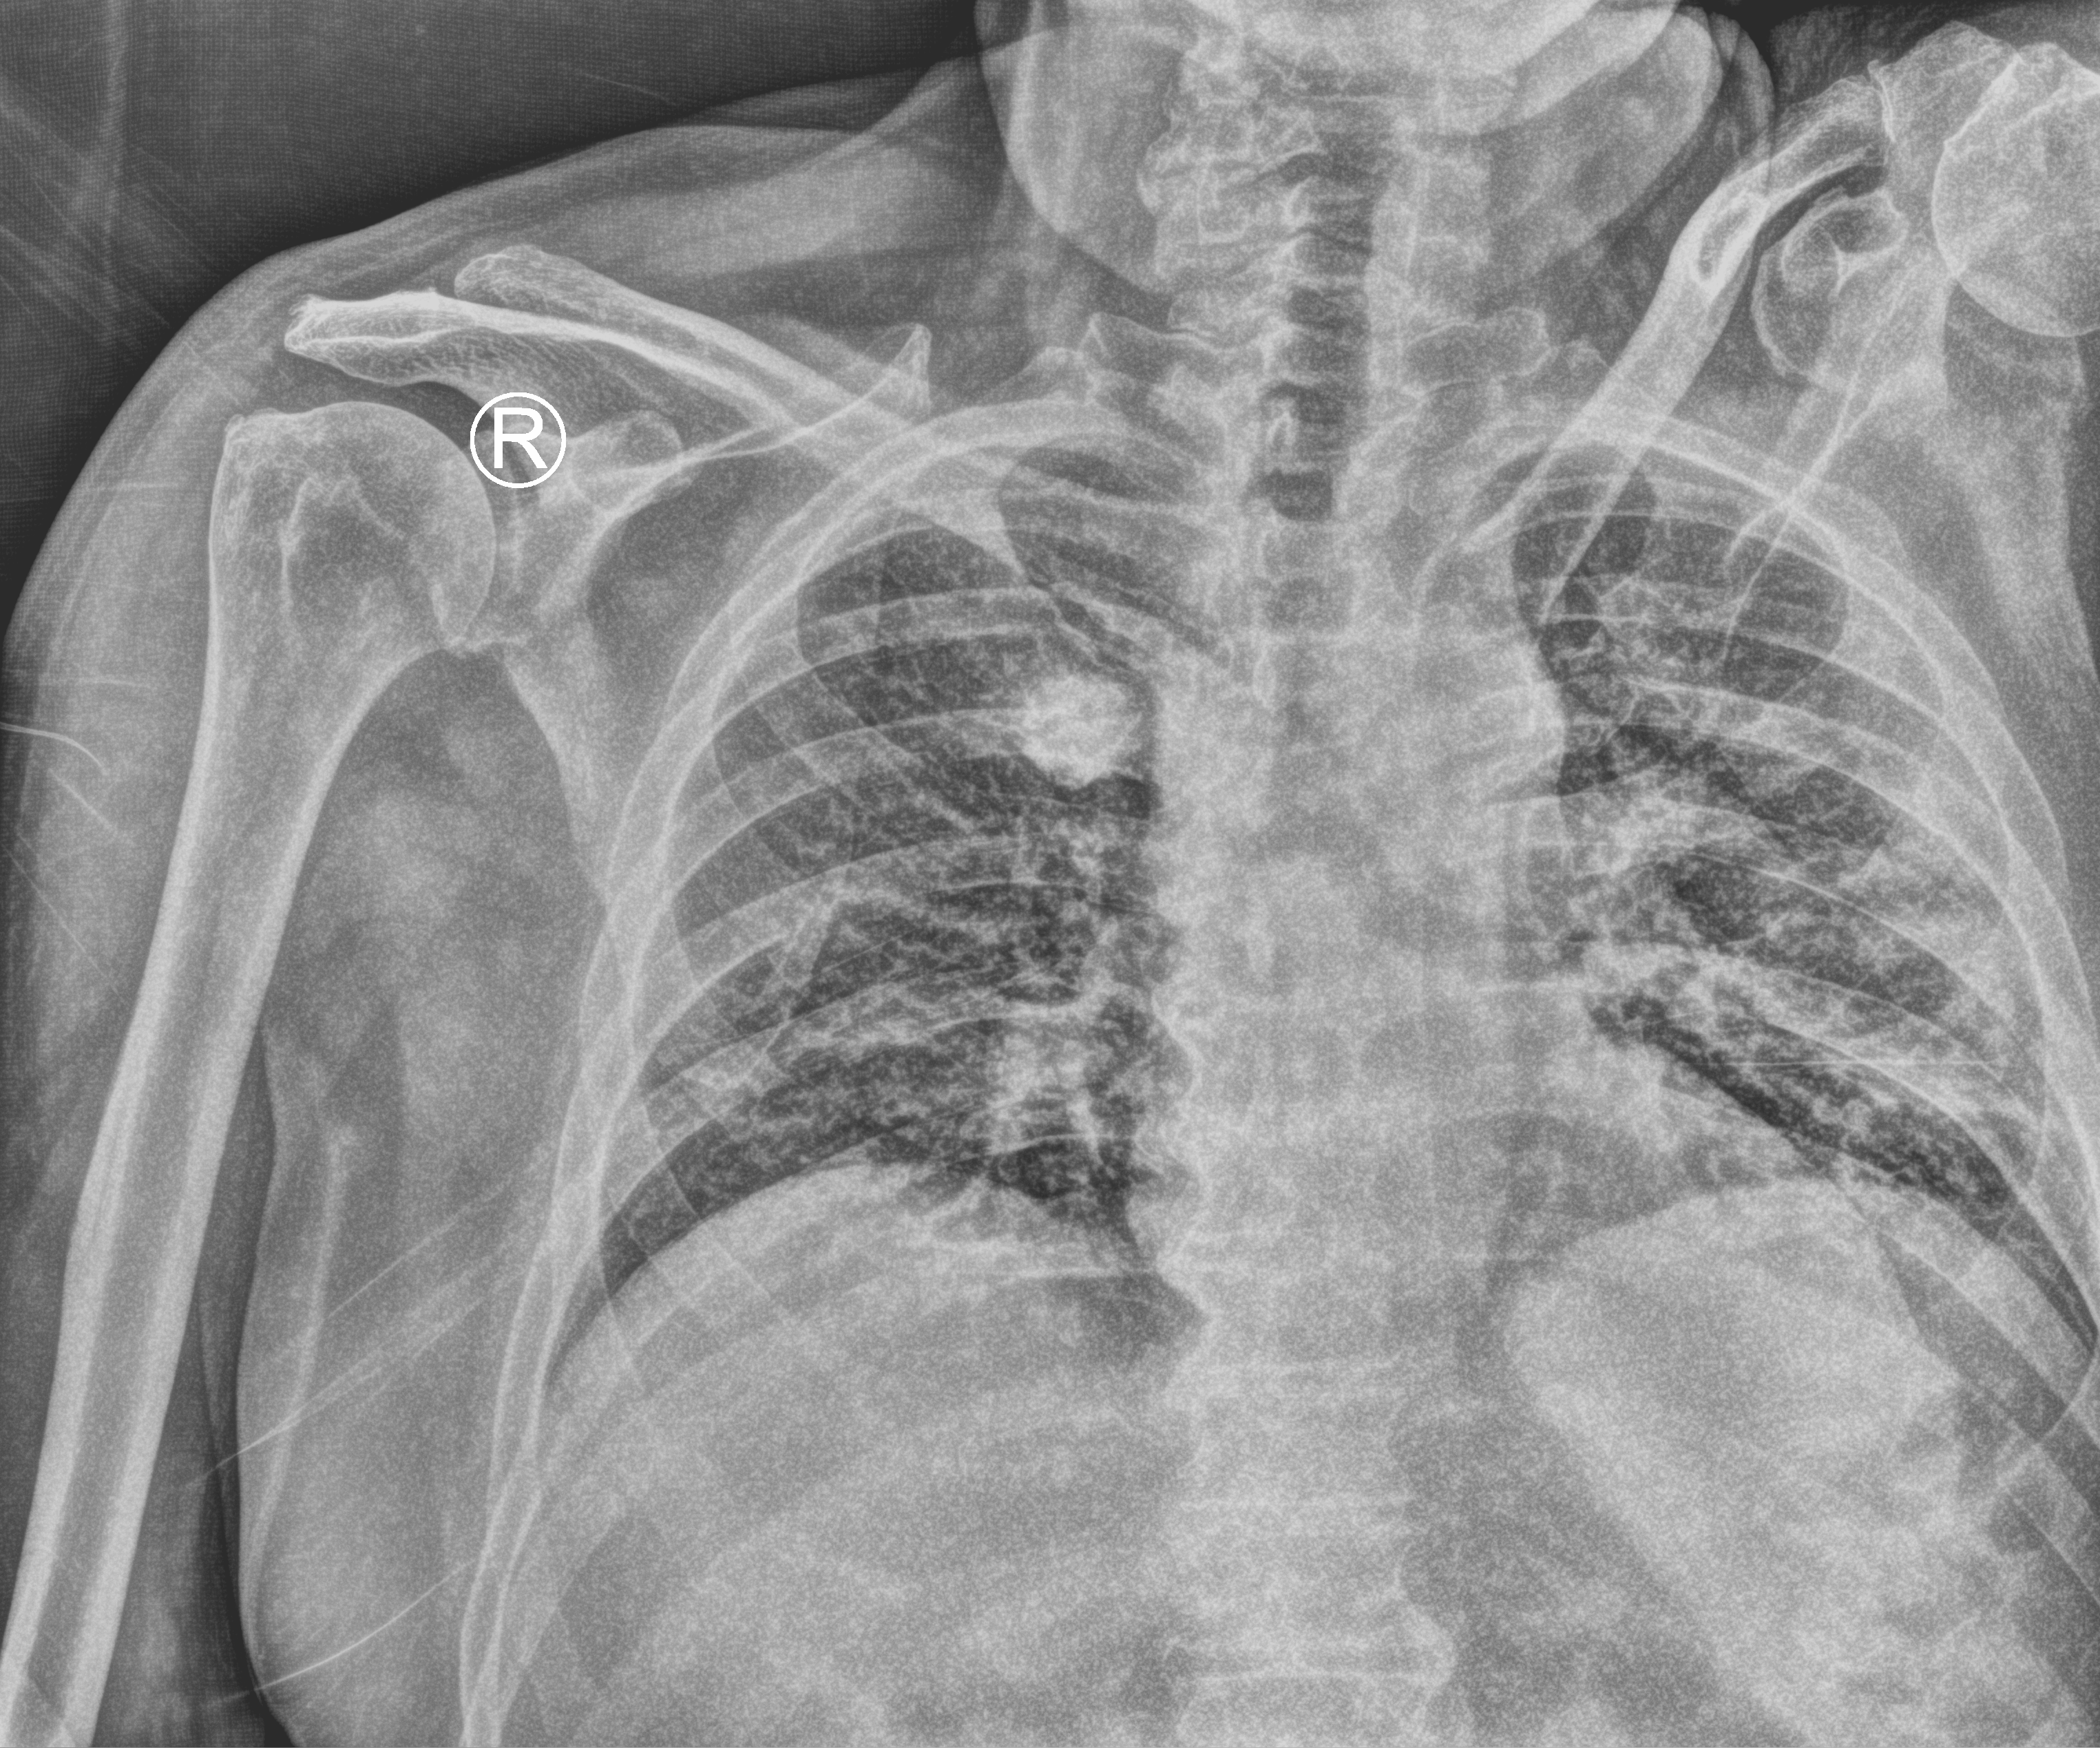
Chest X-ray (portable), anteroposterior (AP) projection. Male patient hospitalised with COVID-19, age 75–90 years.
Admission-level facts for this patient (not findings on this image; timing relative to this image not recorded): mechanically ventilated during this hospital stay: no; admitted to intensive care during this hospital stay: no.